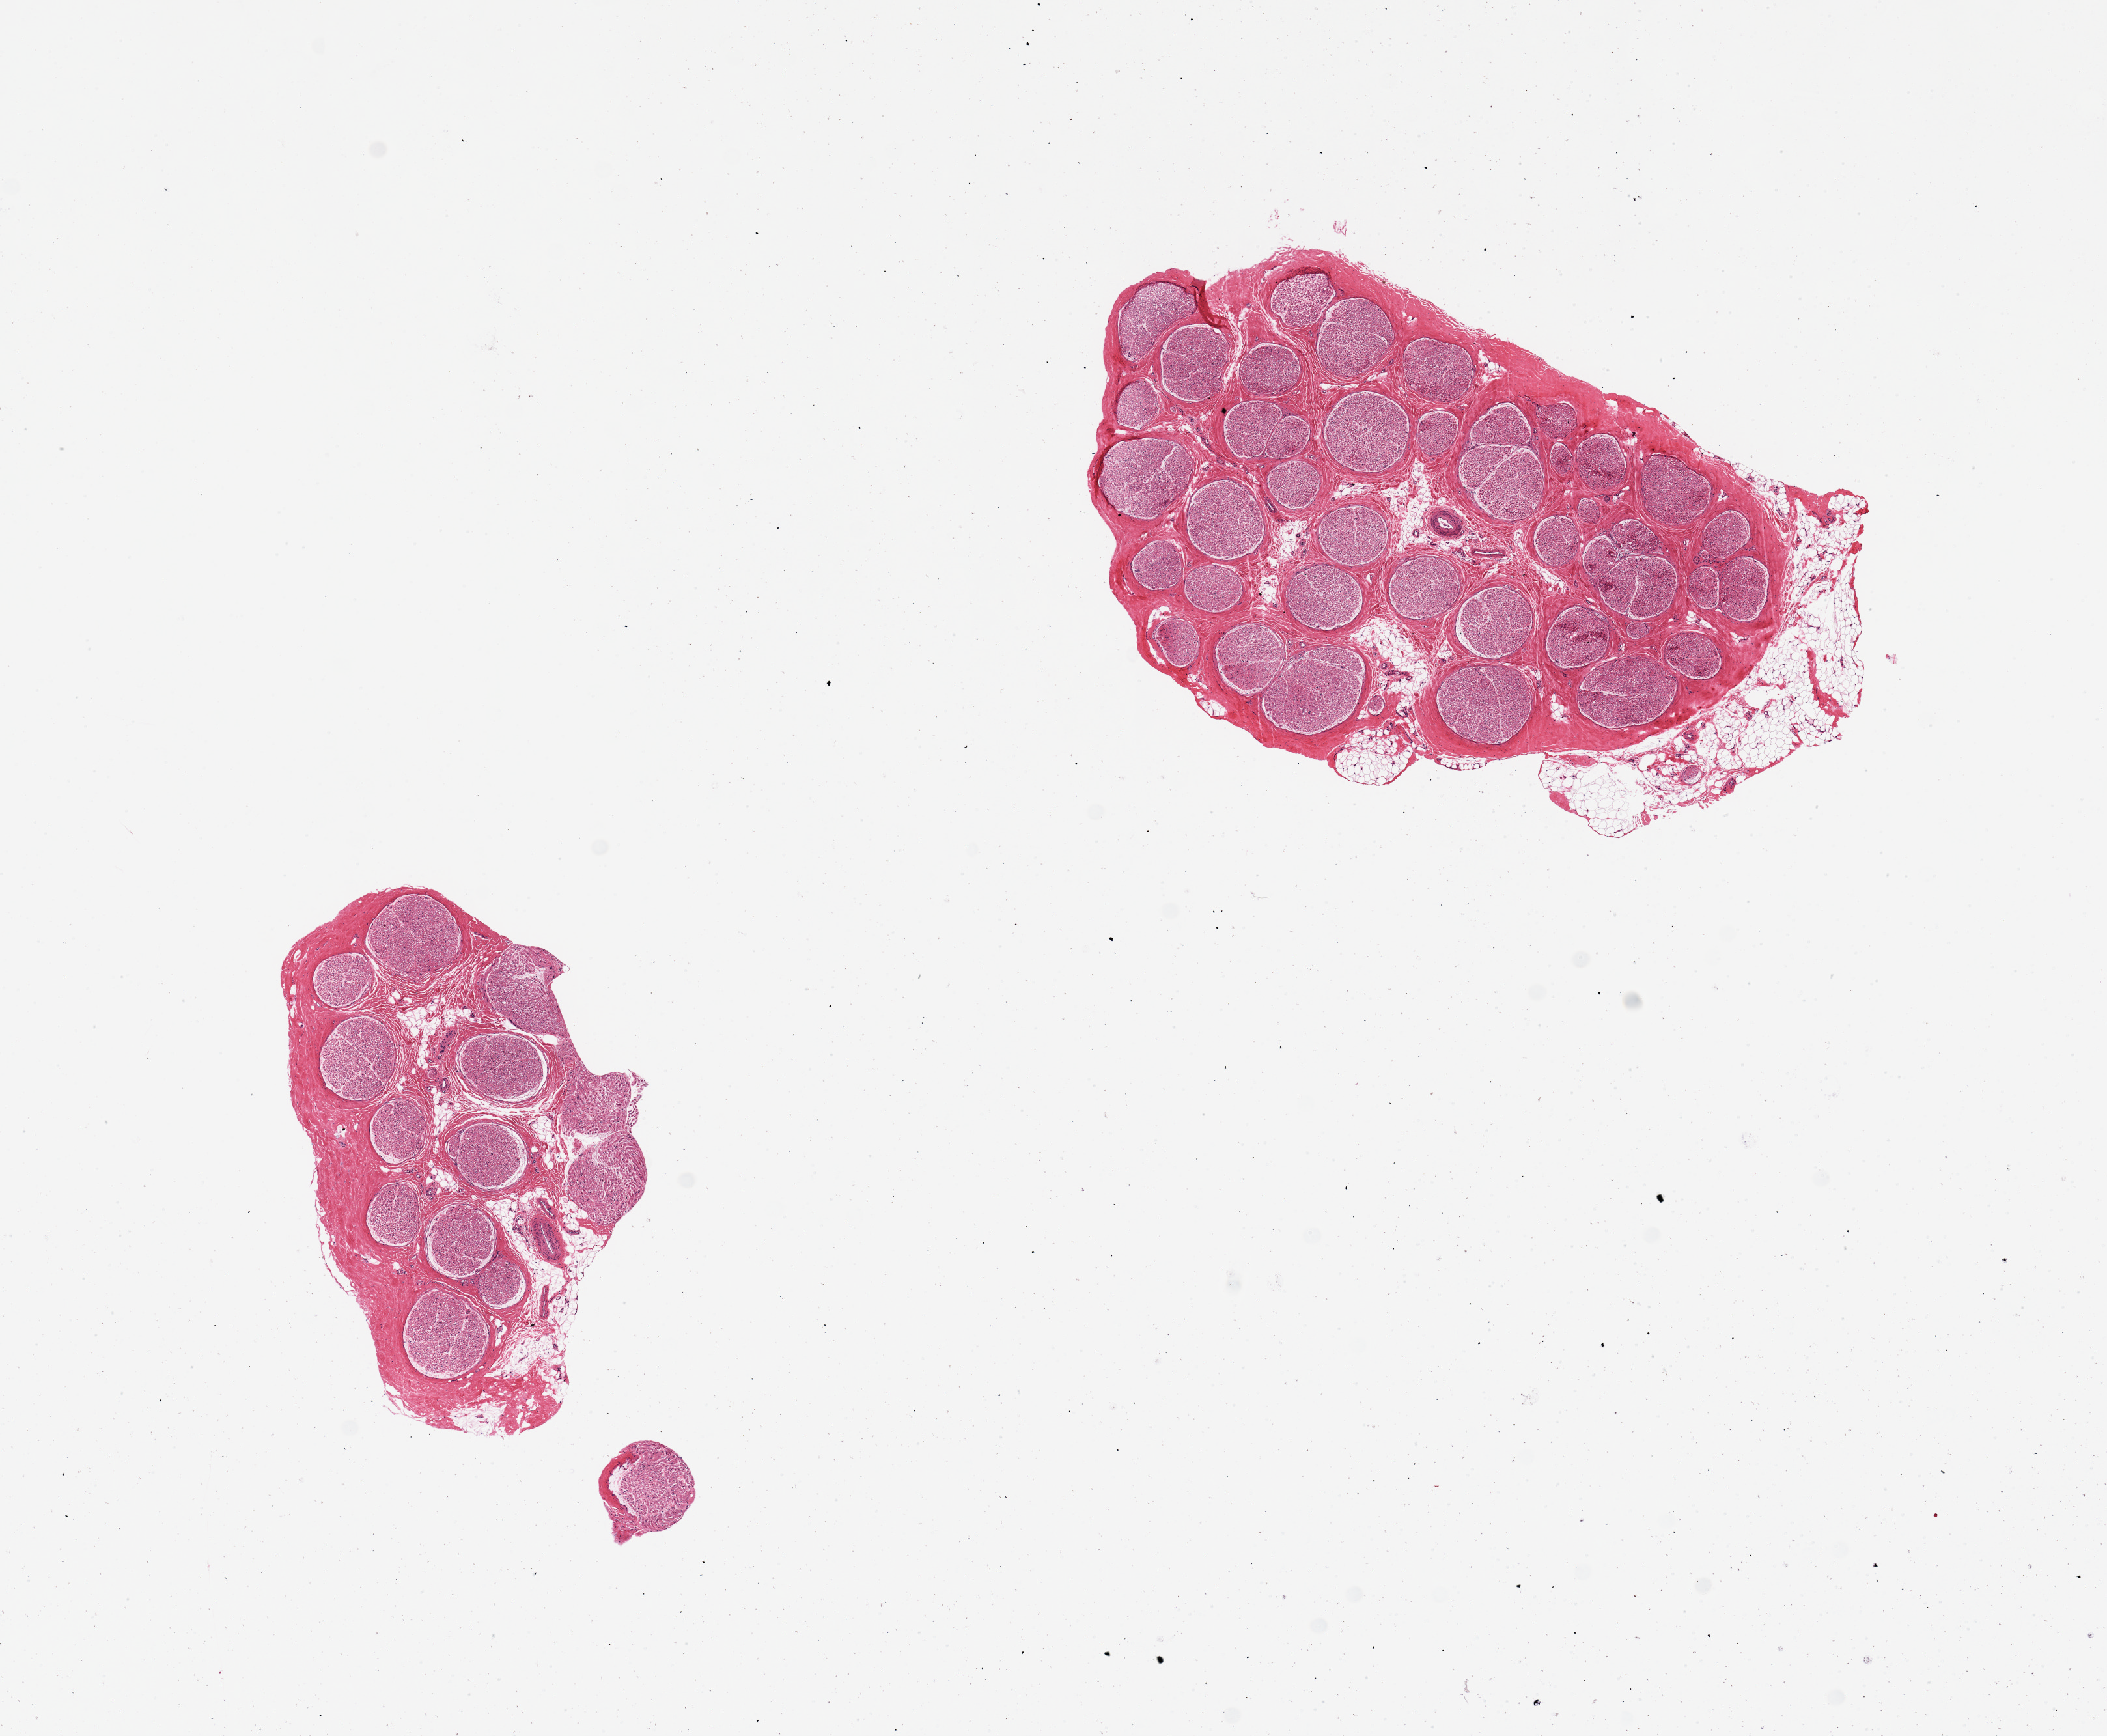
H&E whole-slide image, shown as a low-resolution overview of the whole scanned area (about 12.8 x 10.5 mm, from a 20x scan). PAXgene-fixed, paraffin-embedded tissue. Target tissue: tibial nerve. Donor tissue sample. Donor: male.
Review note (as recorded): 2 pieces, 1 with 20%, other with 10% external and internal fat.